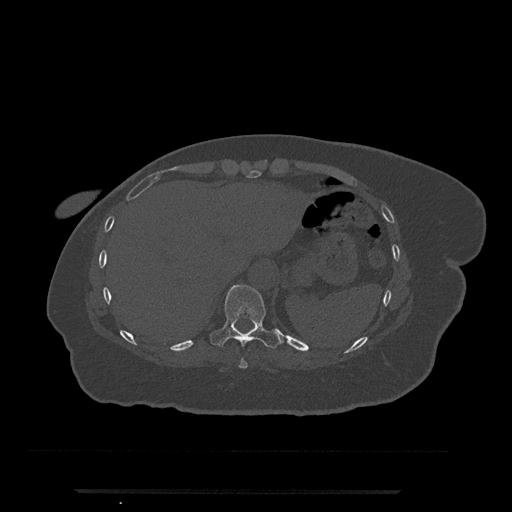
CT including the spine, one axial slice; slice 292 of 797 in the series (ordered by position); reconstruction kernel Br40s/3; 120 kVp; bone window (W 1800 / L 400 HU); 0.5 mm slice thickness; 512 × 512 image matrix. Female patient, age 51 years. Case-level facts recorded for this patient, not image findings: primary cancer: neuro; vertebrae with lytic lesions (as recorded): T8.
Structures marked on this image (semi-automatically segmented with operator editing):
- T10 vertebra: box from (x=210, y=285) to (x=281, y=349) px
- T9 vertebra: (x=239, y=358)–(x=248, y=369)